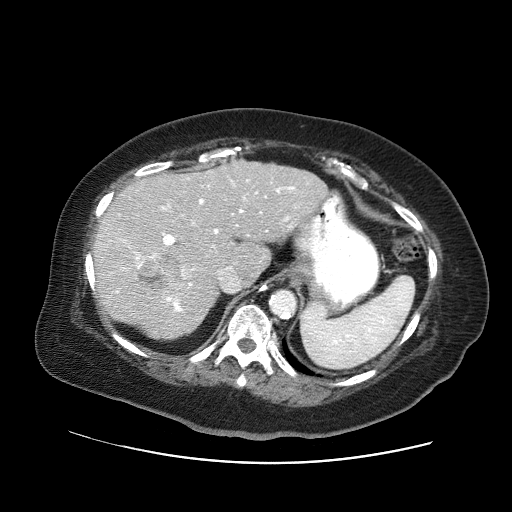
Contrast-enhanced abdominal CT (liver protocol), one axial slice. Position 39 of 71 along the scan axis. Reconstruction kernel STANDARD. Soft-tissue window (W 400 / L 40 HU). 2.5 mm slice thickness. 512 × 512 image matrix, field of view 400 × 400 mm. From the clinical record (not read from this slice): diagnosis: hepatocellular carcinoma (patient treated with transarterial chemoembolisation; whether this scan precedes or follows treatment is not stated here); TNM stage (as recorded): Stage-II; Child-Pugh class: A; tumour differentiation: poorly differentiated; tumour nodularity: multinodular.
Outlined on this slice (semi-automatically segmented with operator editing):
- liver parenchyma outside the tumour (the mass and vessels are separate outlines, so this box may not span the whole liver): bounding box <92,160,328,338> (left, top, right, bottom; pixels)
- mass: <136,253,180,291>
- liver vessels: <105,178,296,312>